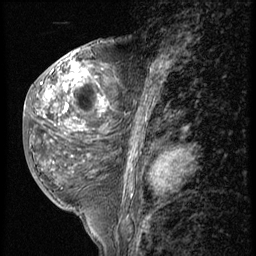
Breast MRI (dynamic contrast-enhanced), one sagittal slice. Slice 26 of 56 in the series (ordered by position). 3 images stored at this slice position (order not interpretable as contrast timing). 1.5 T. TE 4.2 ms, TR 9 ms. 2.5 mm slice thickness. 256 × 256 image matrix, field of view 180 × 180 mm. Patient: female, 50 years. From the clinical record (not read from this slice): setting: breast cancer imaged before/during neoadjuvant chemotherapy; receptor status: triple-negative.
Outlined on this slice (semi-automatic segmentation, software-assisted and operator-edited):
- analysis volume of interest (the breast-tissue region the enhancement analysis was run in; not a lesion): box from (x=25, y=50) to (x=117, y=191) px
- tumour enhancement mask (voxels above the 140 % enhancement threshold inside the analysis volume of interest): (x=40, y=63)–(x=109, y=113)